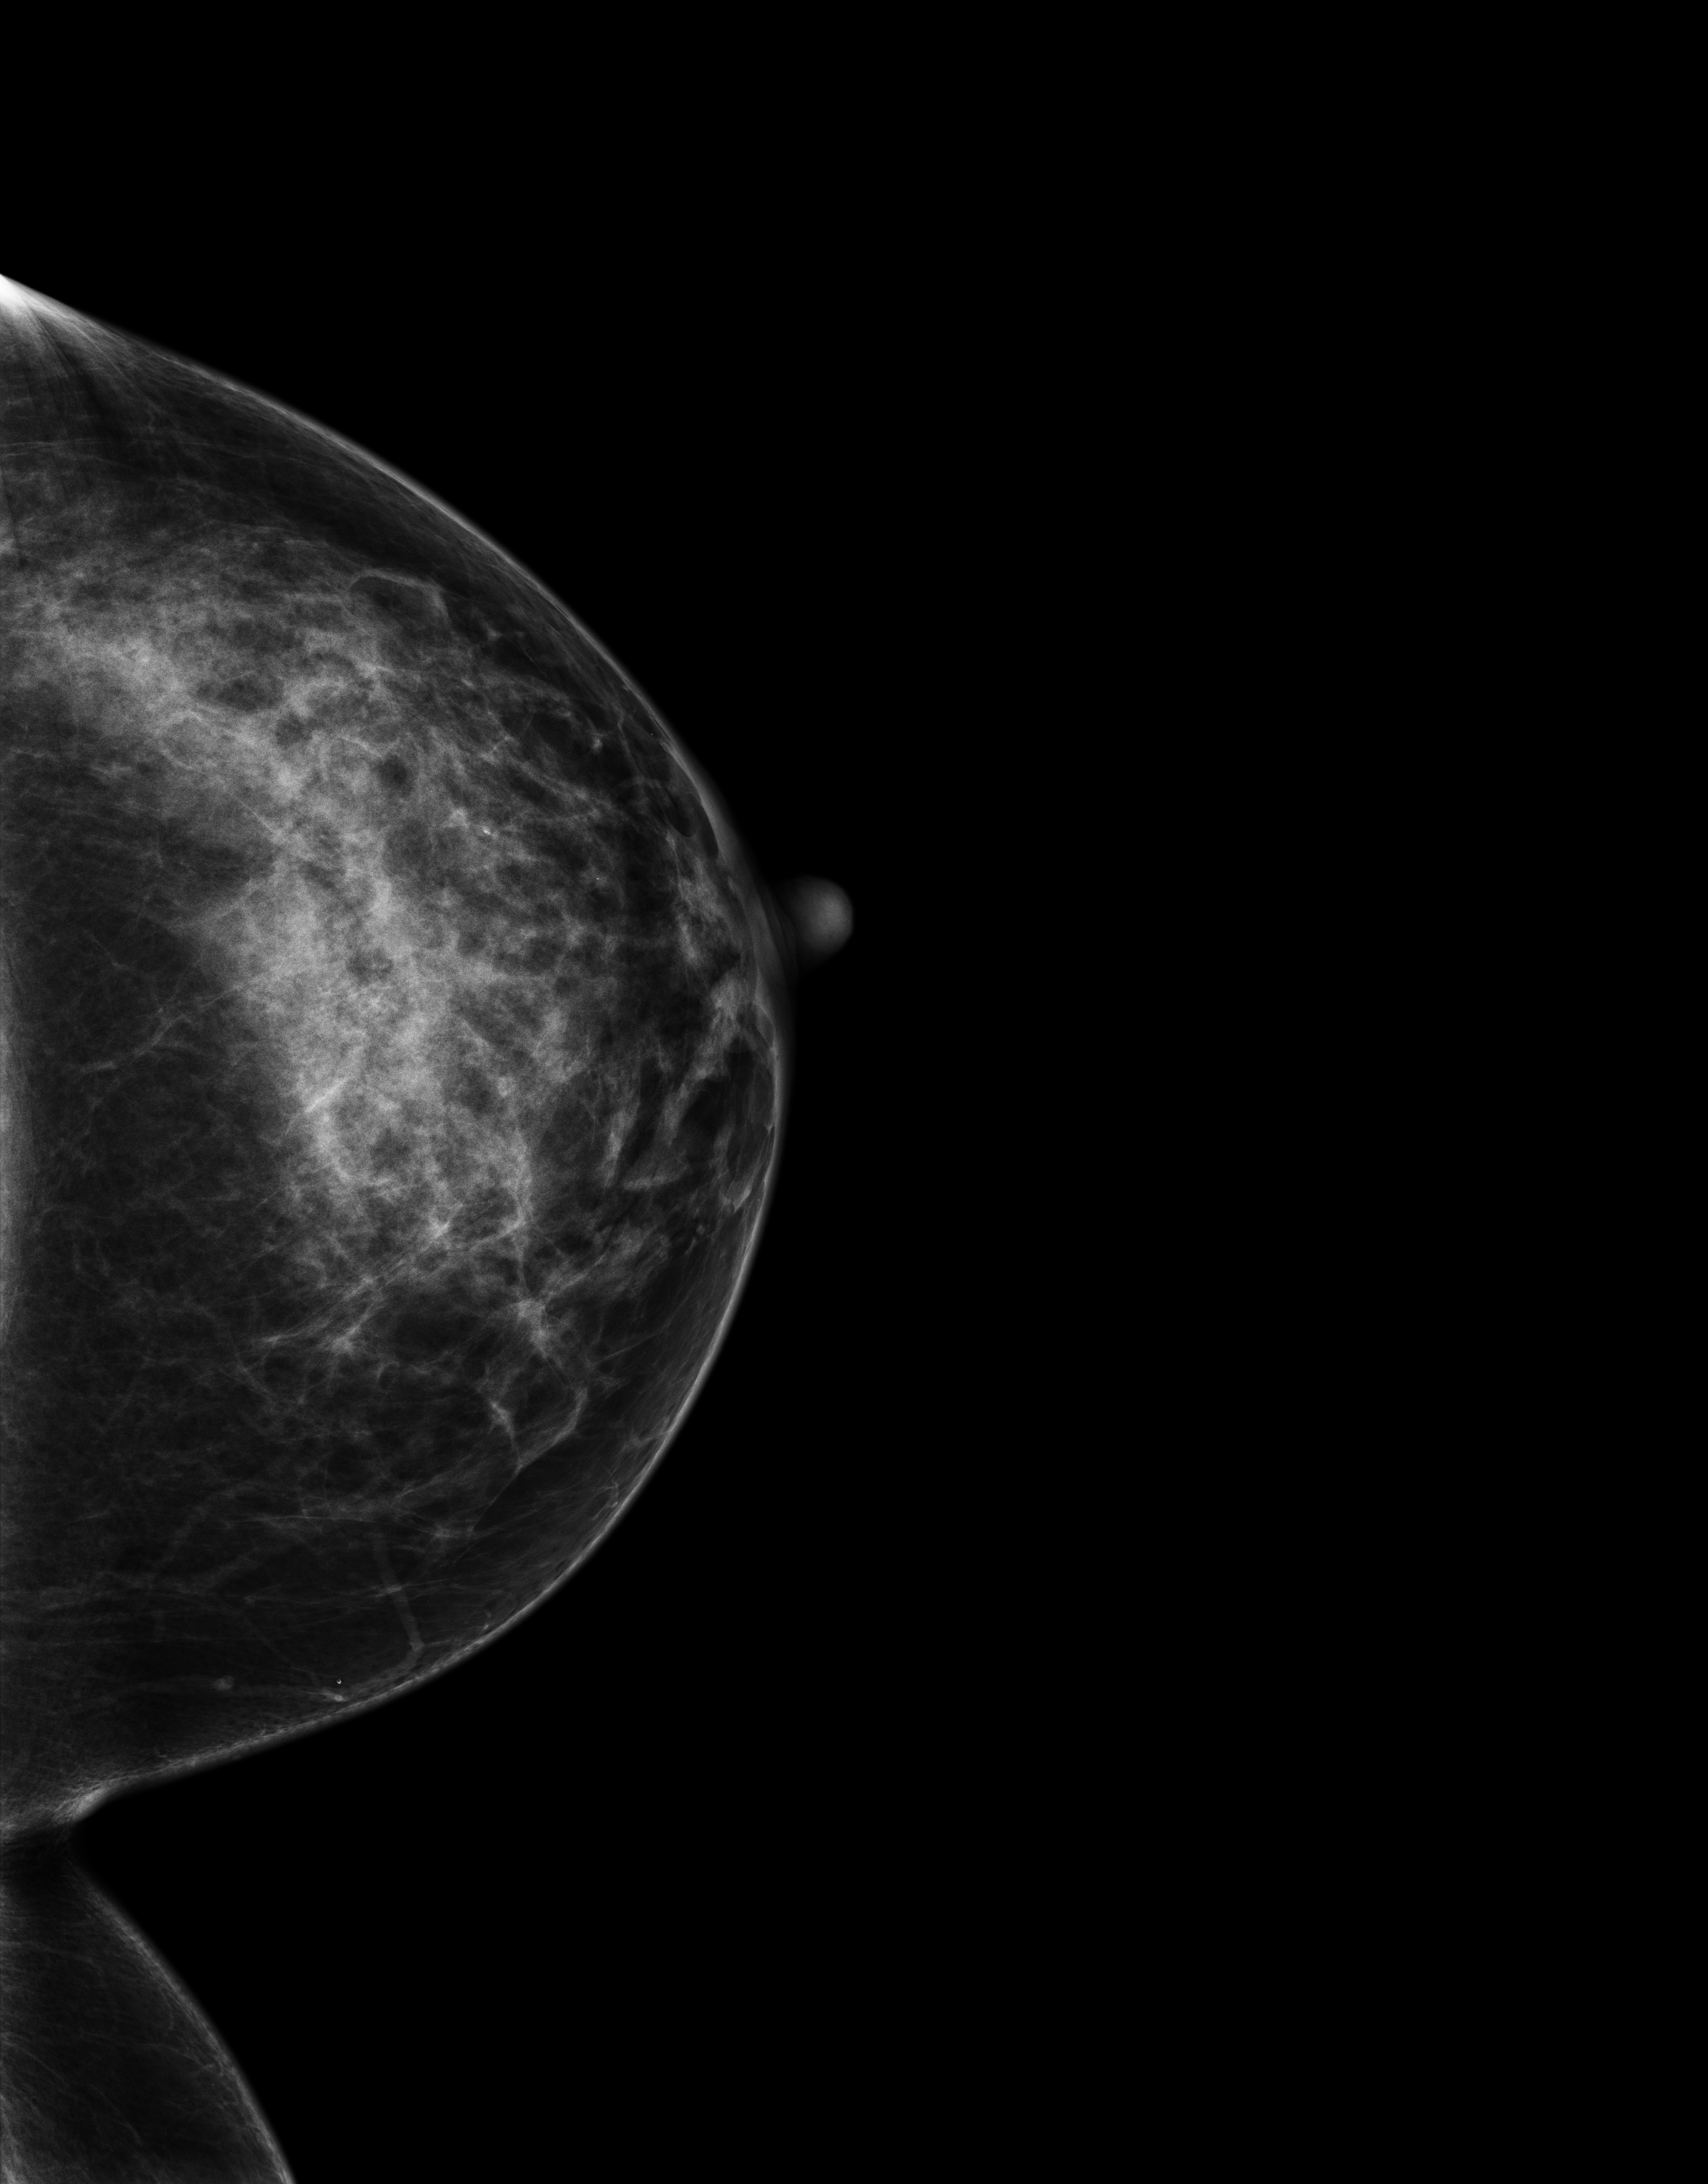
Screening examination, compressed breast thickness 65 mm. Patient: female, 50 years.
Image type: full-field digital mammogram. Breast: left. Projection: cranio-caudal projection.